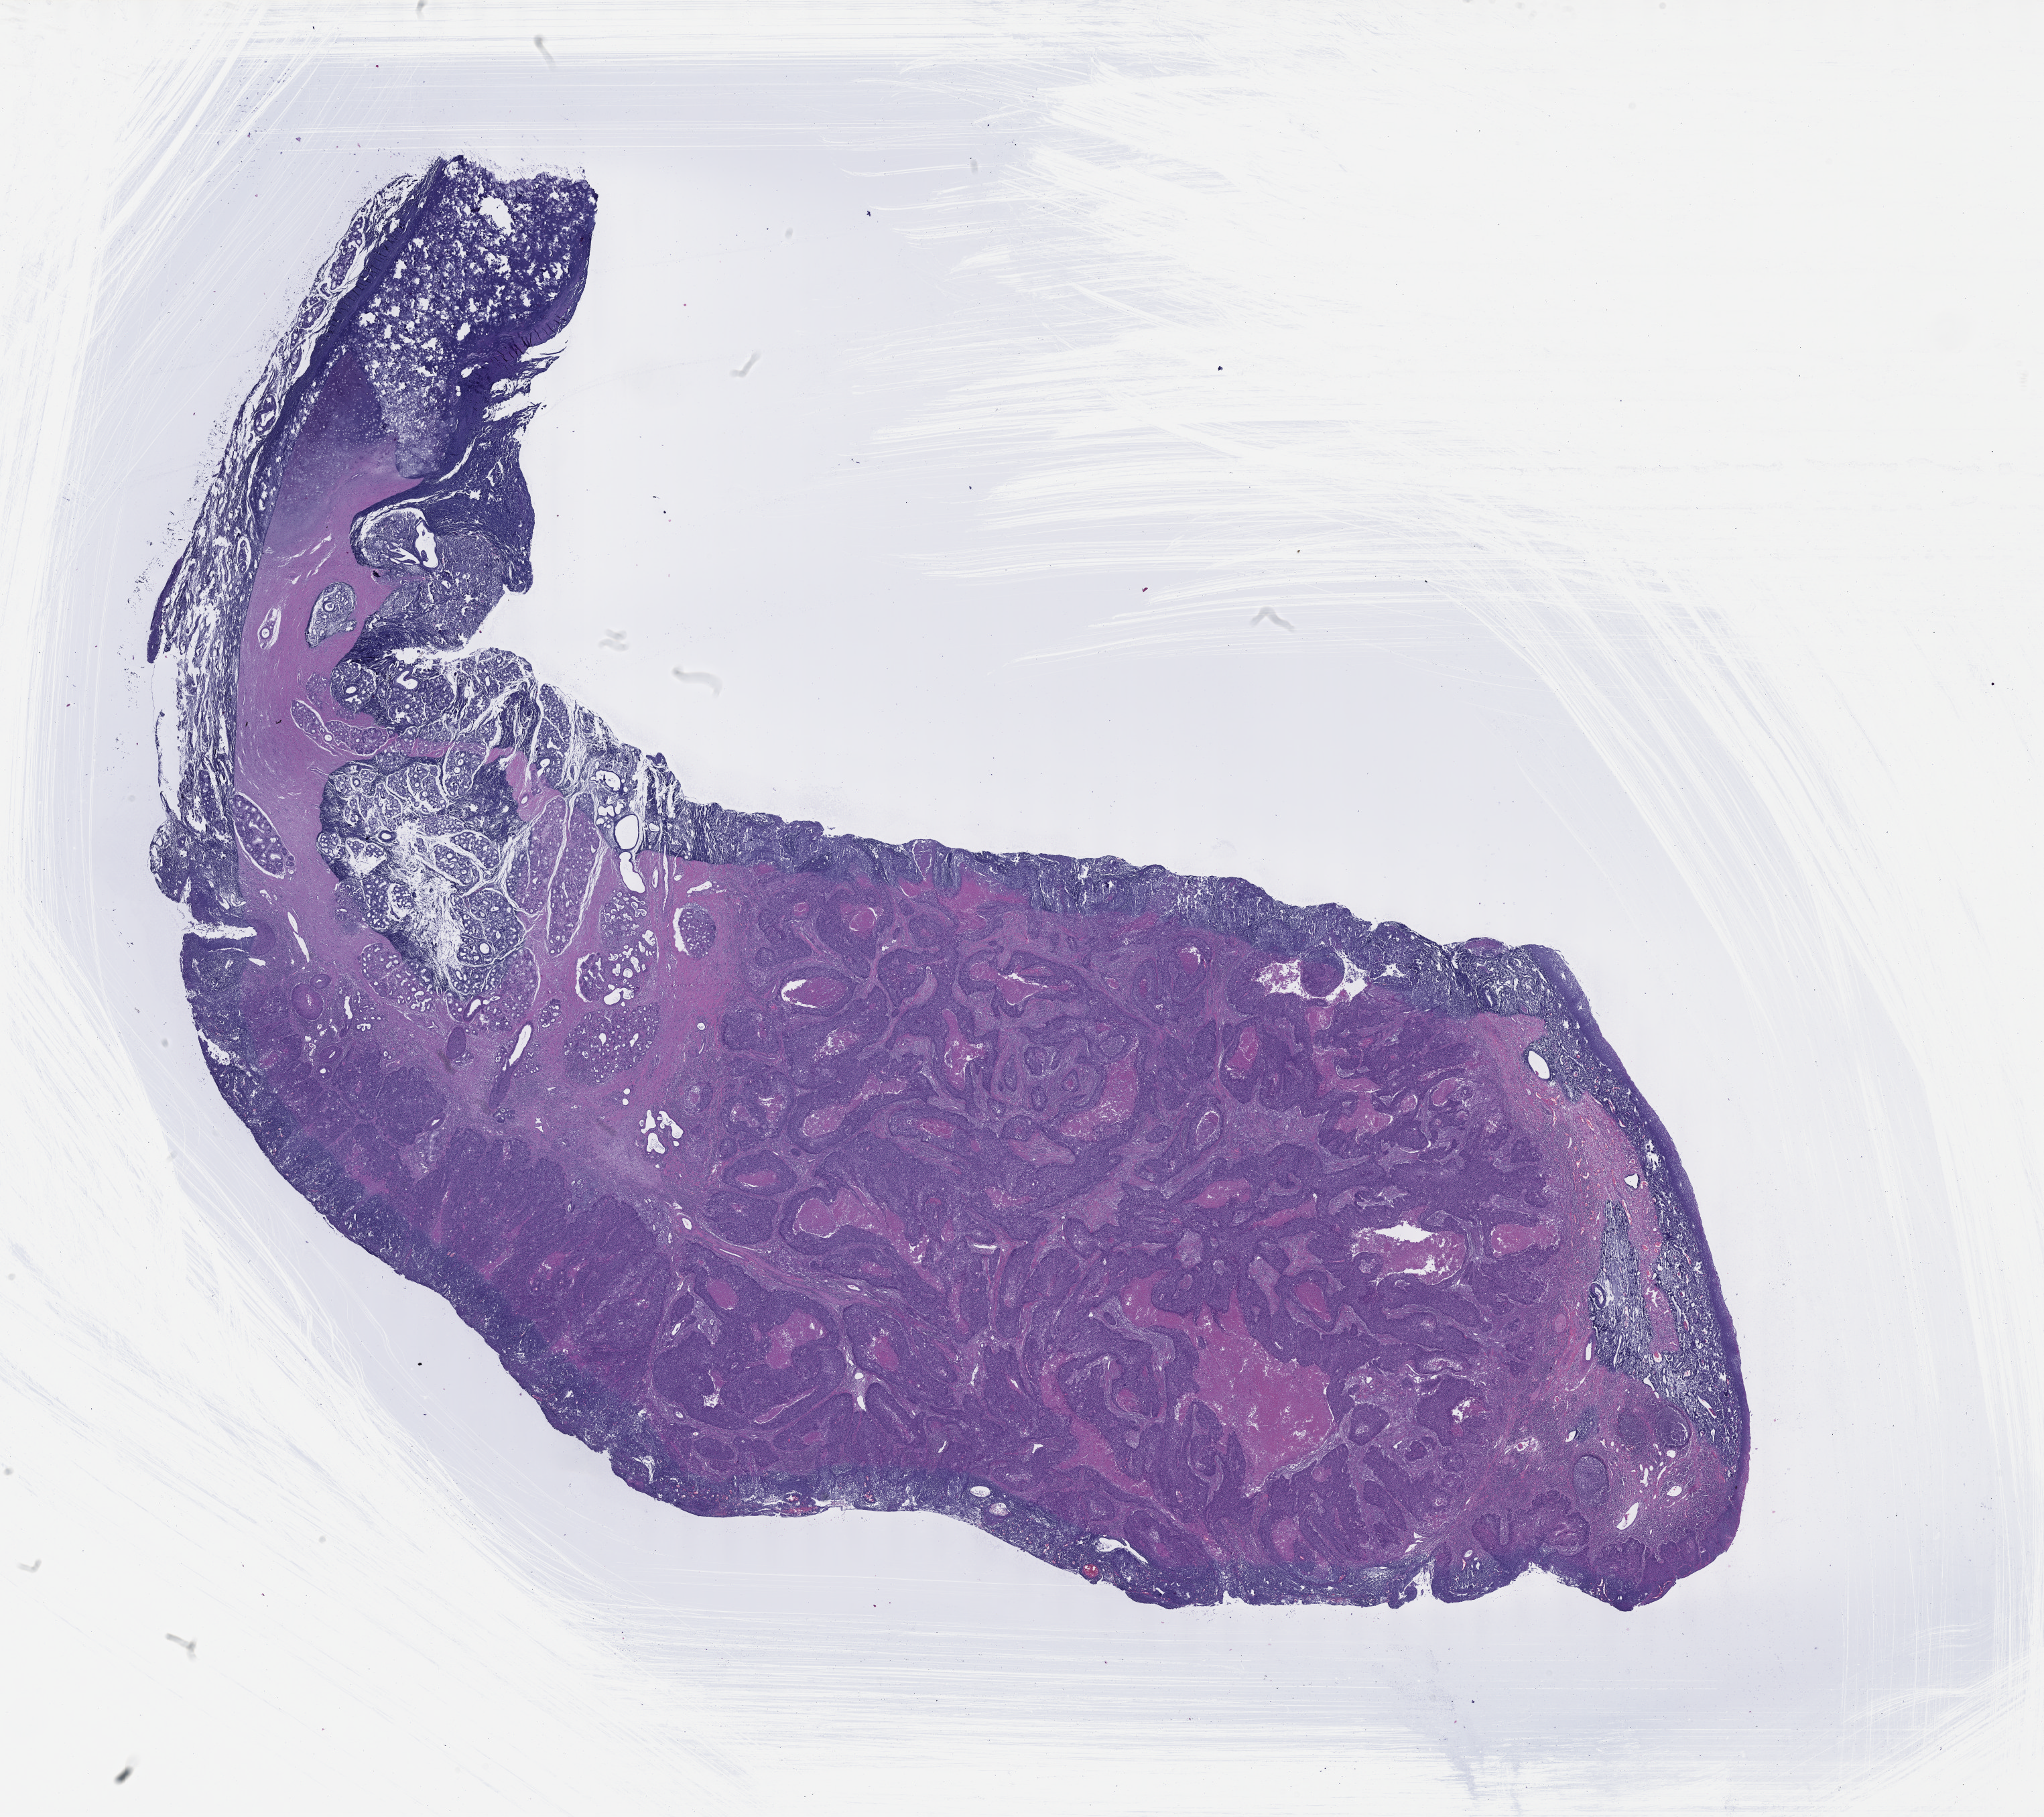
H&E-stained whole-slide image — a low-resolution overview of the entire scanned area, about 24.6 x 21.9 mm. Formalin-fixed paraffin-embedded (FFPE) diagnostic section. Primary tumour sample from the head and neck. Male, age 75 years at initial diagnosis. Histologic grade: G2 (moderately differentiated).
- diagnosis: Squamous cell carcinoma, NOS (larynx, NOS)
- AJCC pathologic stage: II (5th edition)